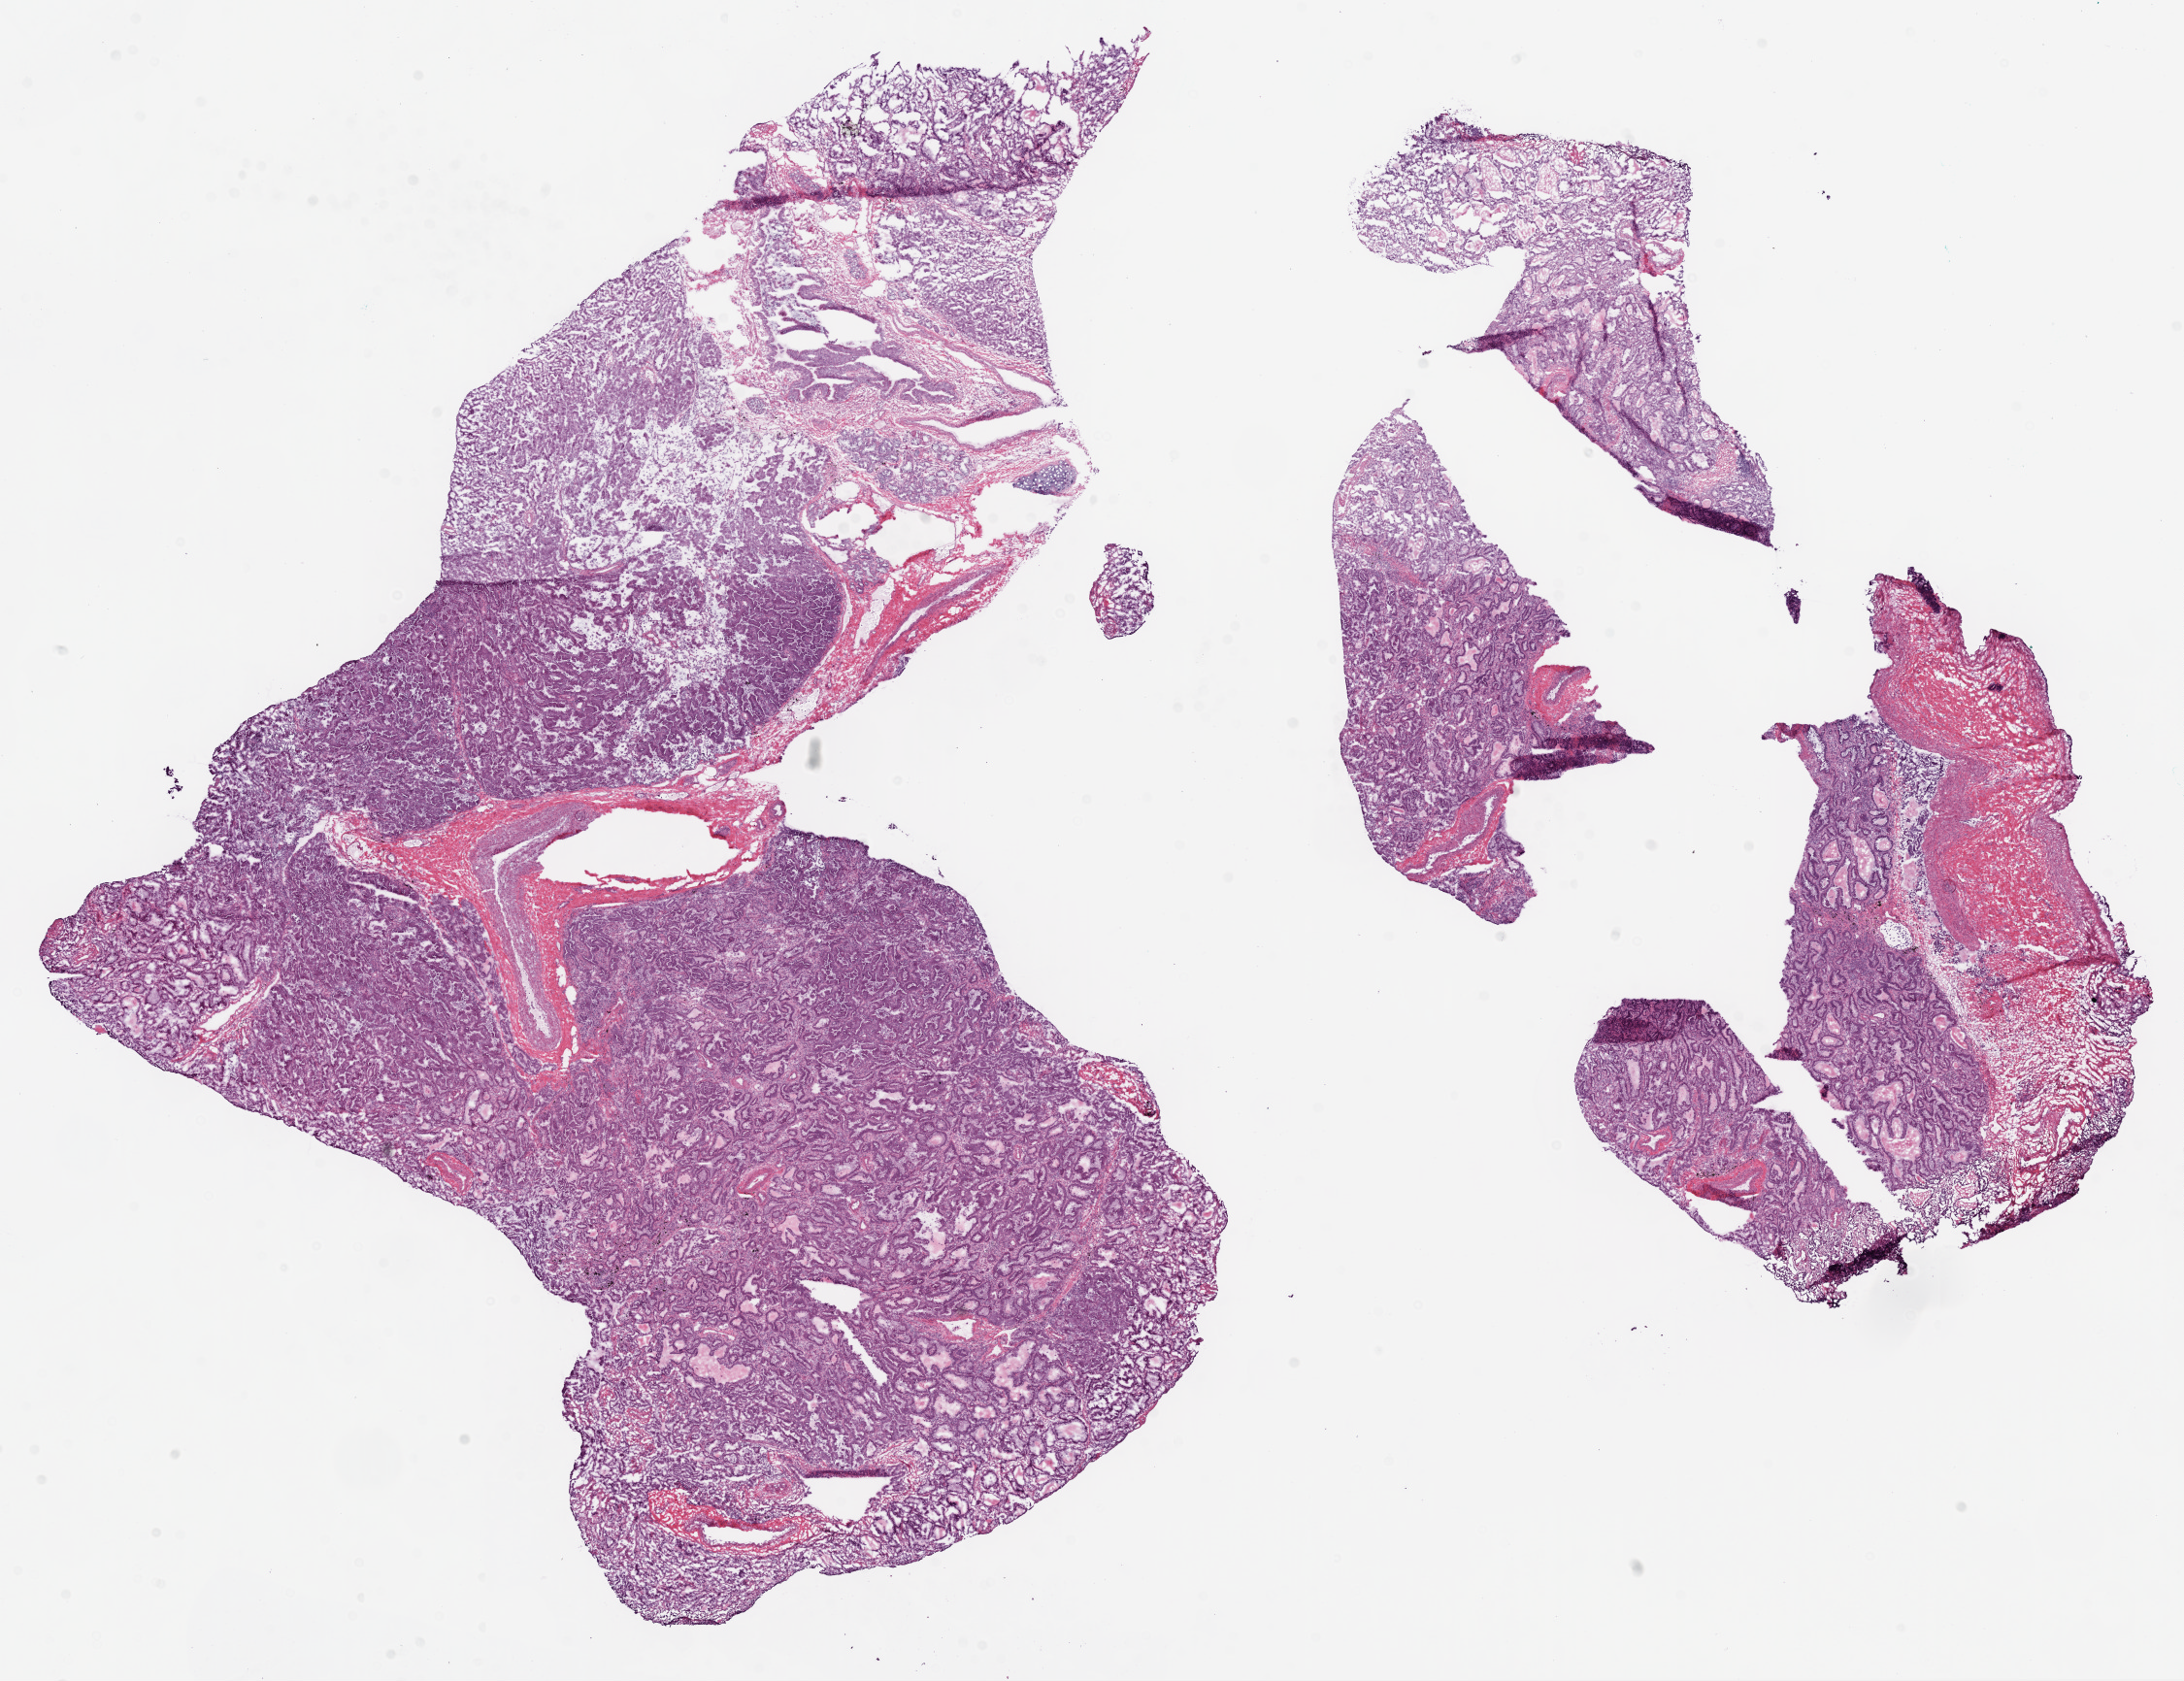
H&E whole-slide image, low-resolution overview of the scanned area, about 18.1 x 13.9 mm (slide scanned at 20x); frozen section from the bottom of the tissue portion; sample: primary tumour, lung. Patient: male, age at initial diagnosis 63 years. Slide review estimates, as recorded: tumour cells 77%, tumour nuclei 90%, normal cells 0%, stromal cells 15%, necrosis 8%.
Laterality: right. AJCC pathologic stage: IV (6th edition). Diagnosis: Adenocarcinoma with mixed subtypes (overlapping lesion of lung). TNM: T2a N2 M1.